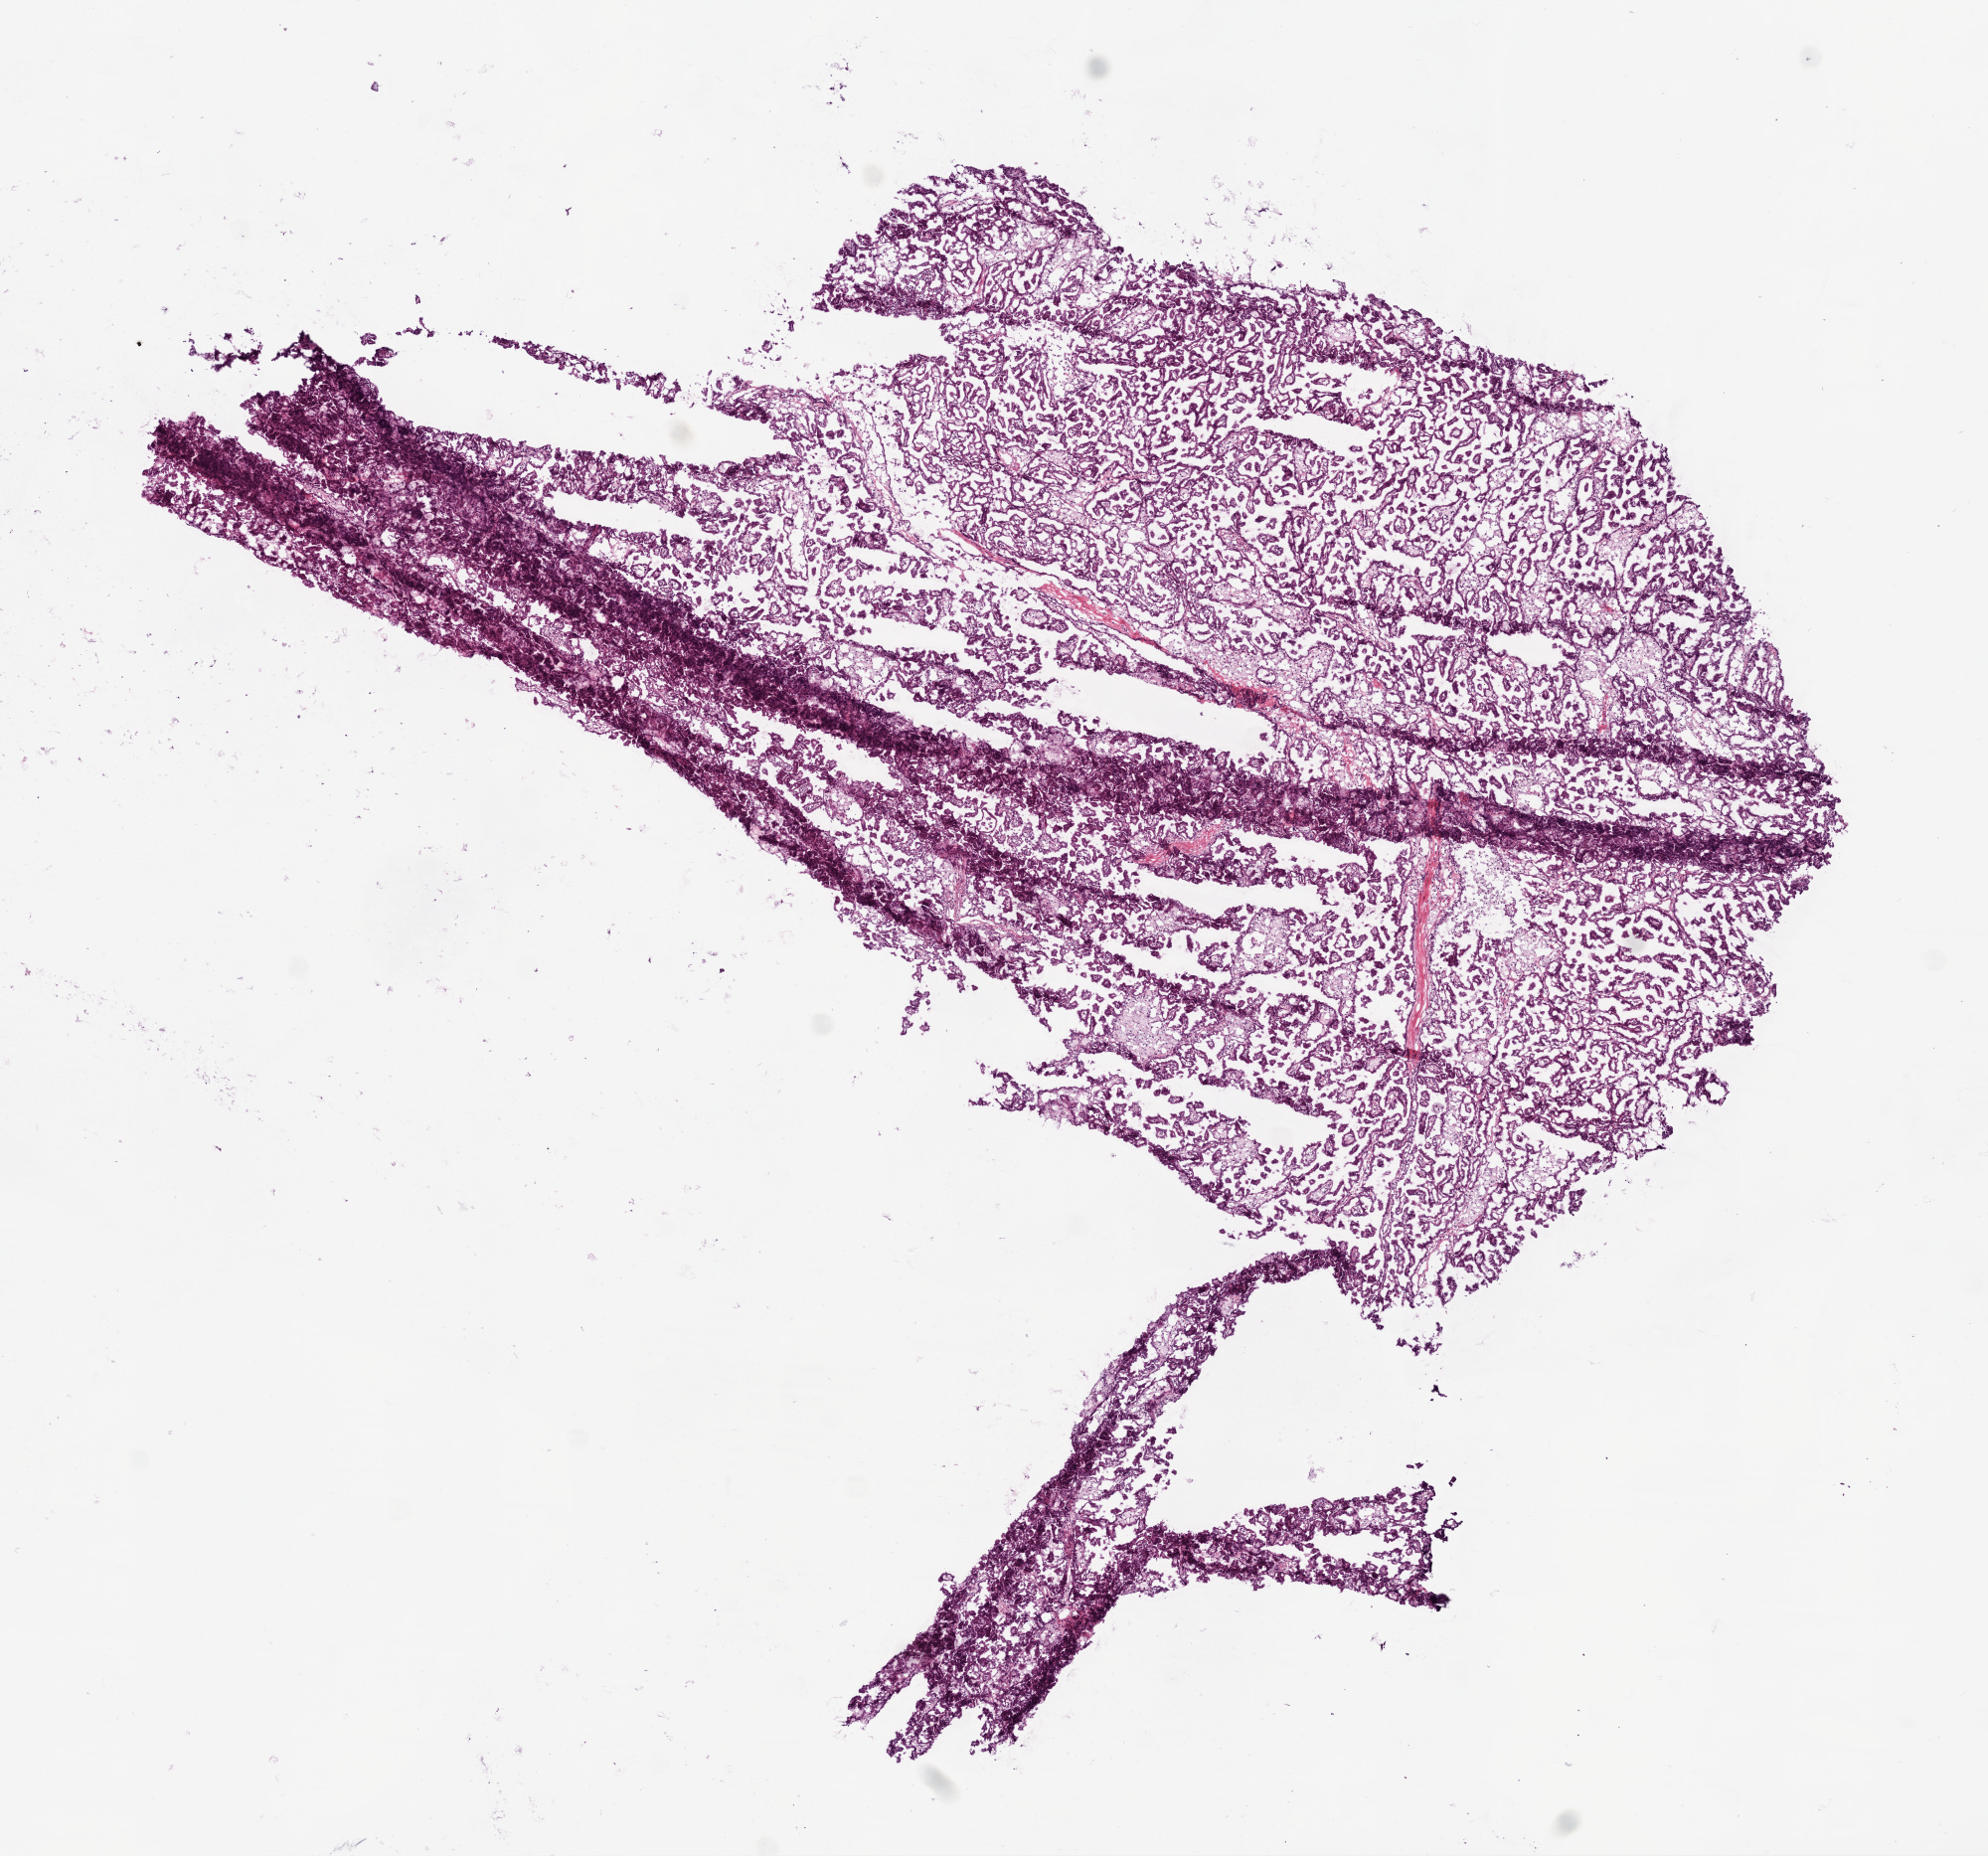
Hematoxylin and eosin (H&E) stained whole-slide image, whole scanned area (about 8.0 x 7.5 mm, slide scanned at 20x) shown as a low-resolution overview. Frozen section. Sample: primary tumour, kidney. Patient: male, age at initial diagnosis 49 years. Pathologist review of this section (percent, as recorded): tumour cells 78%, tumour nuclei 75%, normal cells 0%, stromal cells 20%, necrosis 2%.
* laterality: left
* pathologic diagnosis: Papillary adenocarcinoma, NOS